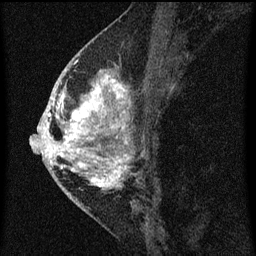
Breast MRI (dynamic contrast-enhanced), one sagittal slice. Position 30 of 60 along the scan axis. Dynamic contrast-enhanced series, image 2 of 3 at this slice position (ordered by acquisition). 1.5 T. TE 4.2 ms, TR 8 ms. 256 × 256 image matrix. Patient: female, 46 years.
Outlined on this slice (semi-automatic segmentation, software-assisted and operator-edited):
- analysis volume of interest (the breast-tissue region the enhancement analysis was run in; not a lesion): box from (x=48, y=68) to (x=132, y=195) px
- tumour enhancement mask (voxels above the 70 % enhancement threshold inside the analysis volume of interest): (x=48, y=68)–(x=132, y=189)